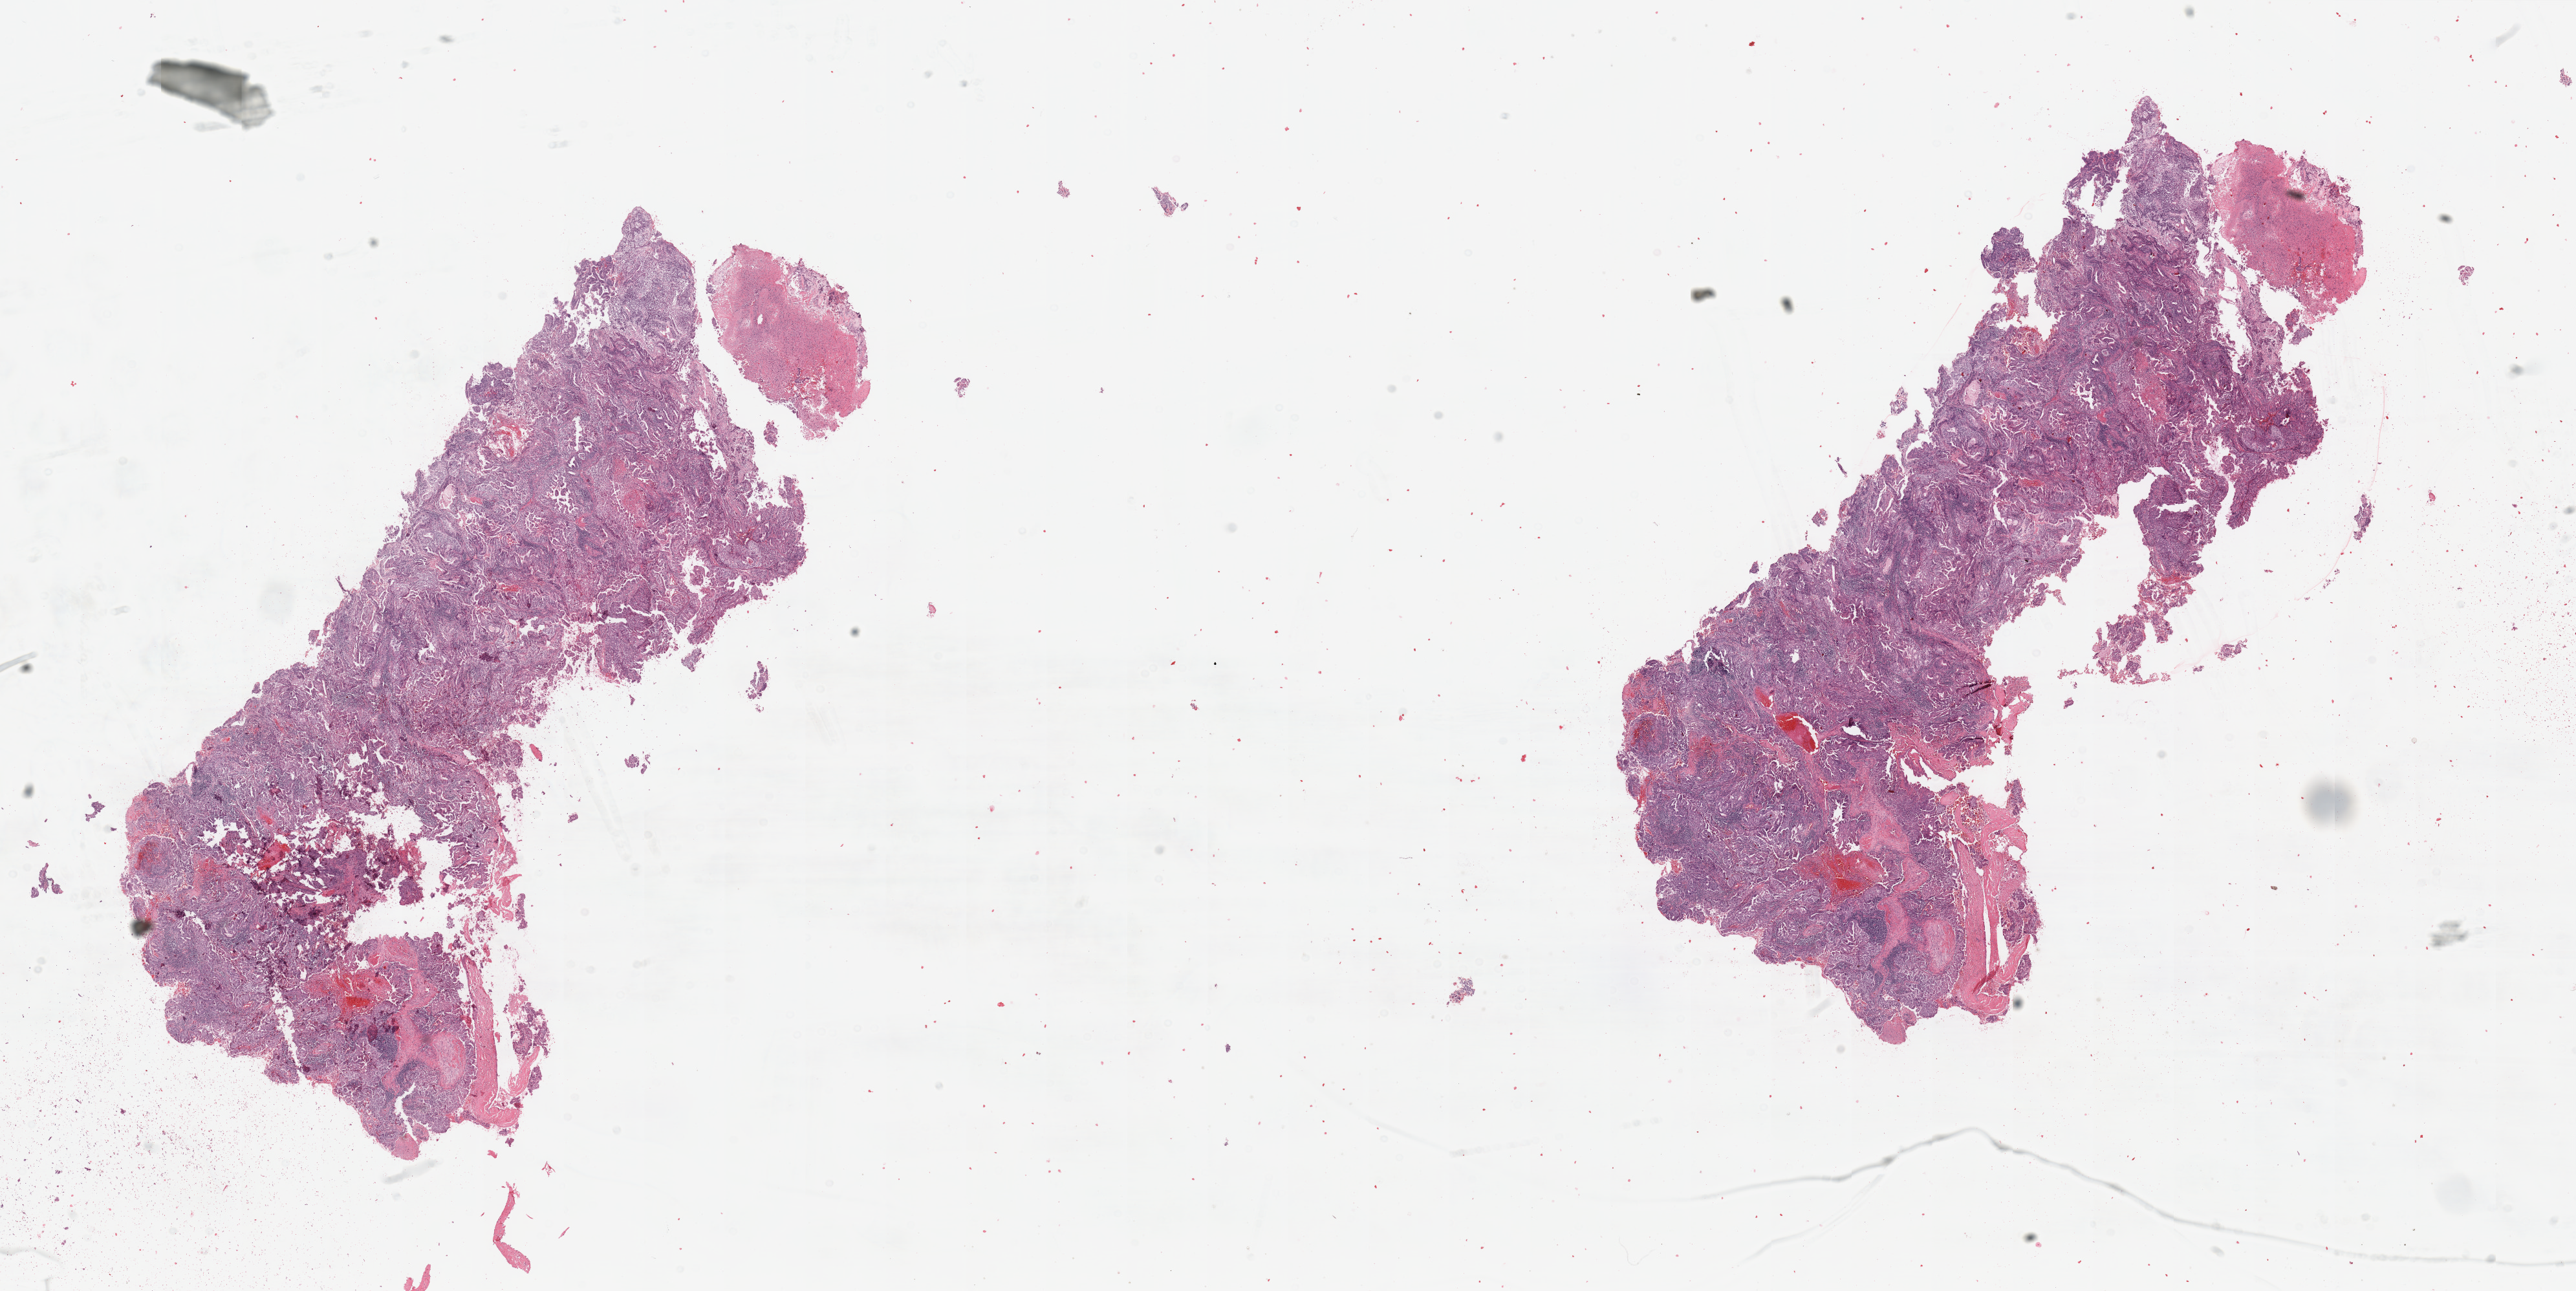
H&E whole-slide image — whole scanned area (about 31.5 x 15.8 mm, from a 20x scan) shown as a low-resolution overview. Uterus, tumour tissue. Female, 51 y/o. Histologic grade: G2 (moderately differentiated).
• AJCC pathologic stage: I
• diagnosis: Endometrioid adenocarcinoma, NOS